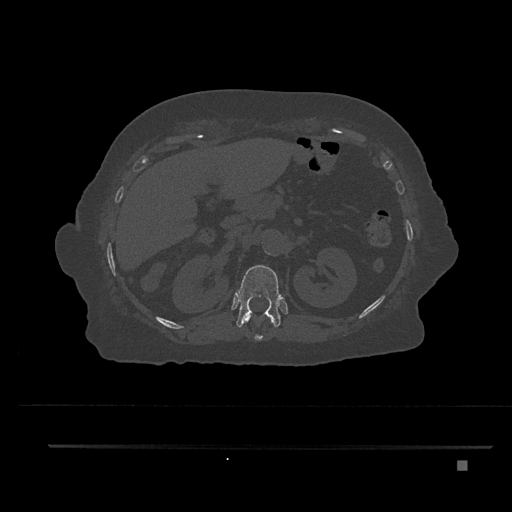
CT including the spine, one axial slice. Slice 275 of 797 in the series (ordered by position). 120 kVp. Bone window (W 1800 / L 400 HU). 0.5 mm slice thickness. 512 × 512 image matrix, field of view 437 × 437 mm. Female patient, age 76 years. From the clinical record (not read from this slice): primary cancer: lung; vertebrae with lytic lesions (as recorded): T11, L3.
Structures marked on this image (semi-automatic segmentation, software-assisted and operator-edited):
- T11 vertebra: bounding box <242,313,273,341> (left, top, right, bottom; pixels)
- T12 vertebra: <236,265,282,328>